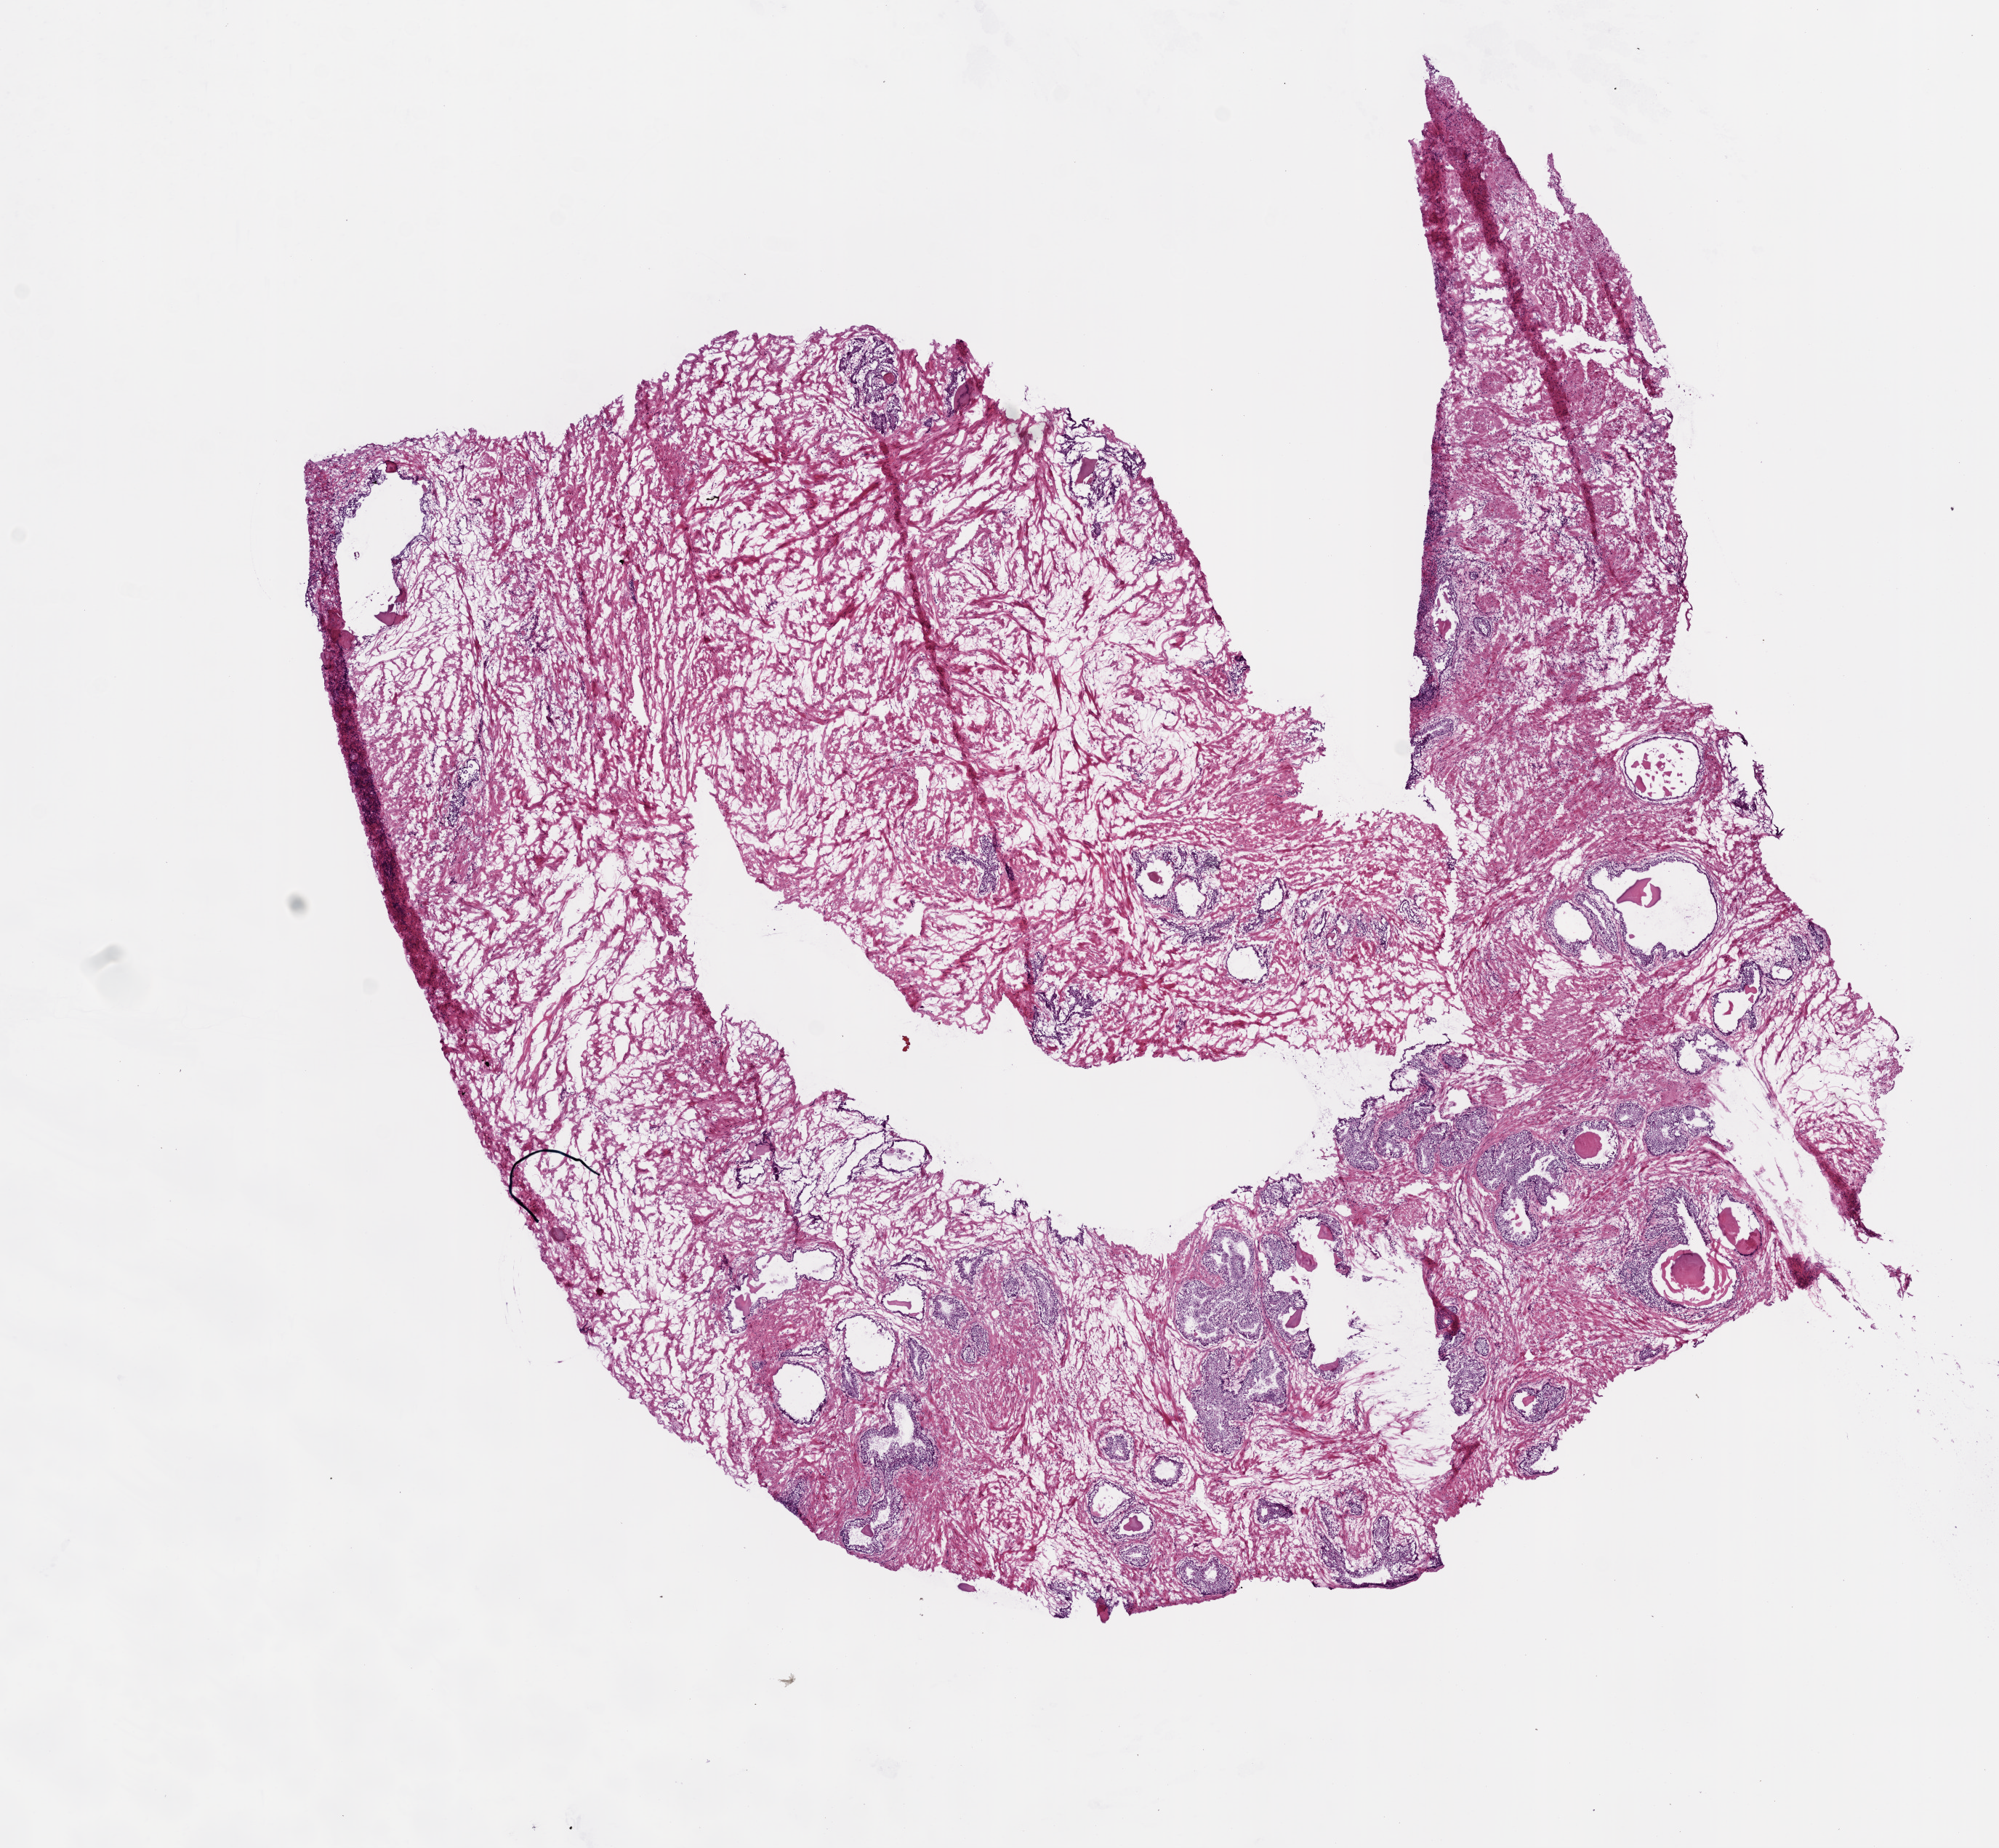
Hematoxylin and eosin (H&E) stained whole-slide image, shown as a low-resolution overview of the whole scanned area (about 11.0 x 10.2 mm), frozen section from the top of the tissue portion, solid tissue normal (non-tumour tissue) sample from the prostate. Male, age 66 years at initial diagnosis.
This section: solid tissue normal sample (biorepository sample class). Patient diagnosis: Acinar cell carcinoma (prostate gland).